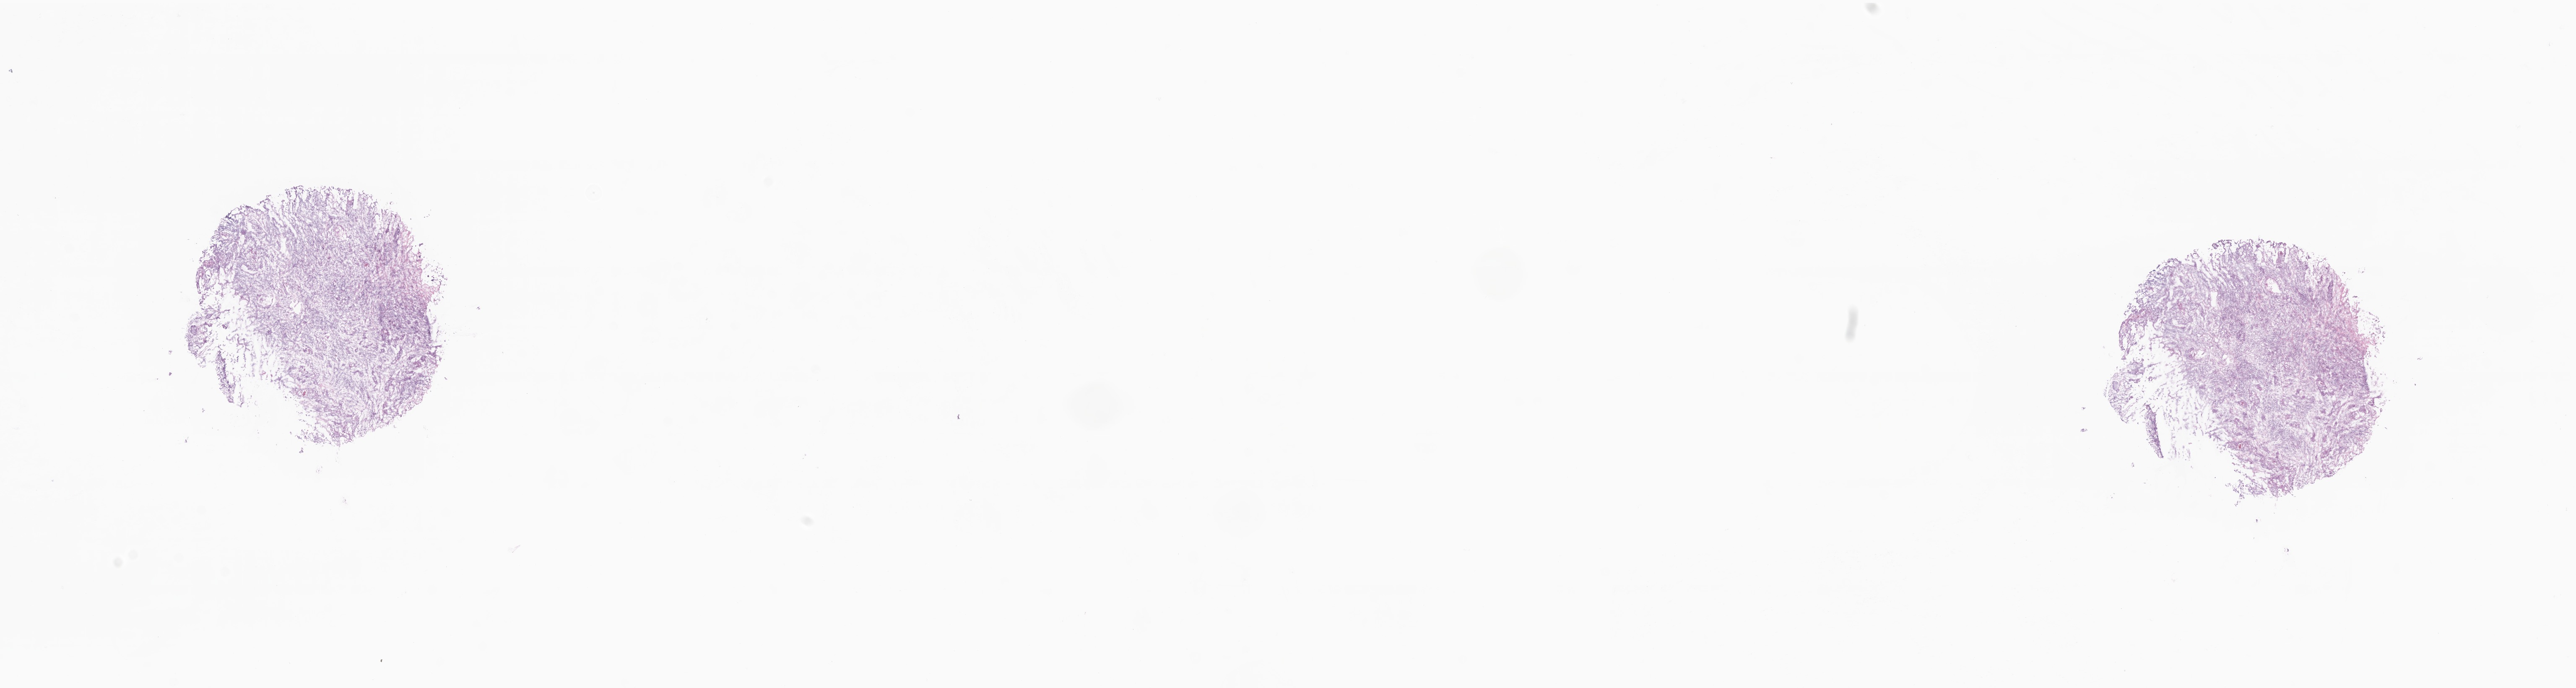
Digitized H&E-stained section, a low-resolution overview of the entire scanned area, about 25.9 x 6.9 mm, frozen section (tissue freezing medium), specimen: primary tumor, site: lower lobe of right lung. Male, age 88 years at initial diagnosis. Composition of this section per pathologist review: tumor cells 95%, tumor nuclei 99%, stromal cells 5%, necrosis 0%, normal cells 0%. Infiltration values recorded for this section: lymphocyte infiltration 0%, monocyte infiltration 0%, neutrophil infiltration 0%.
- section: top of the tissue portion
- histologic diagnosis: Squamous cell carcinoma, NOS